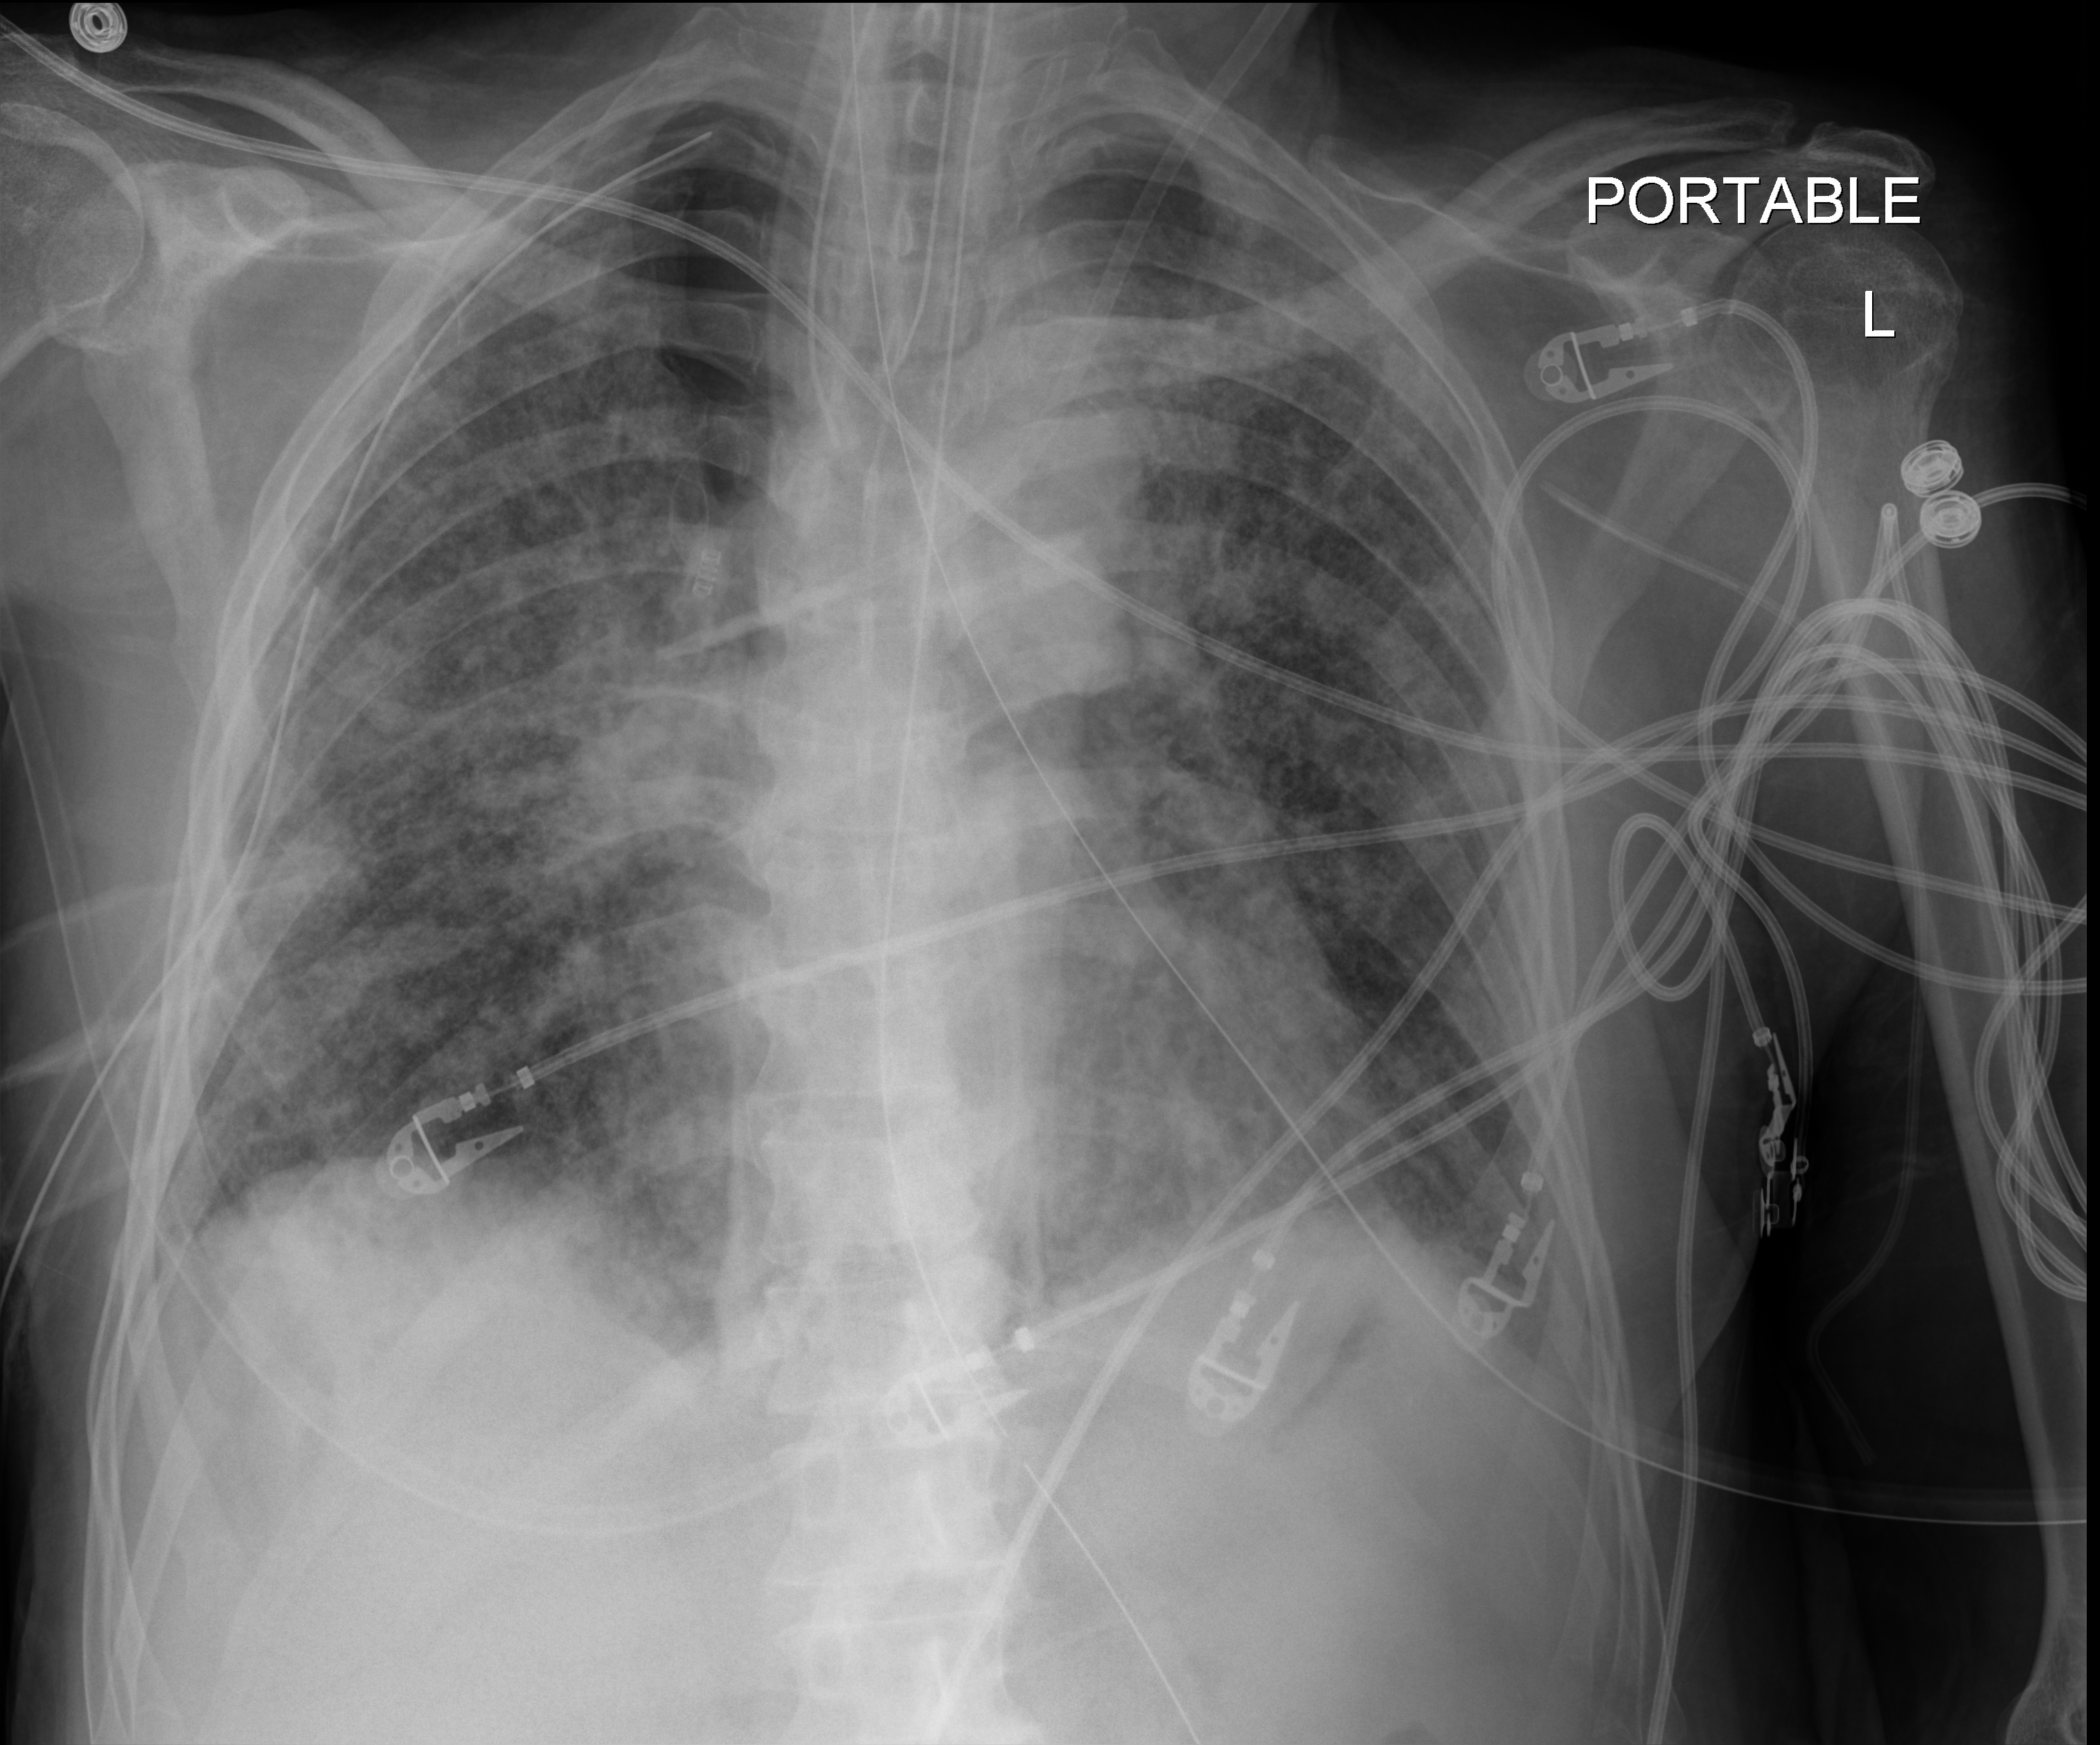
Chest X-ray, anteroposterior (AP) projection. Male patient hospitalised with COVID-19, age 60–74 years.
Admission-level facts for this patient (not findings on this image; timing relative to this image not recorded): admitted to intensive care during this hospital stay: yes; hypertension (admission record): no.